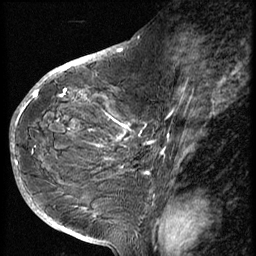
Breast MRI (dynamic contrast-enhanced), one sagittal slice; position 29 of 56 along the scan axis; 3 images stored at this slice position (order not interpretable as contrast timing); 1.5 T; TE 4.2 ms, TR 9 ms; 256 × 256 image matrix, field of view 180 × 180 mm. Patient: female, 49 years. Case-level facts recorded for this patient, not image findings: setting: breast cancer imaged before/during neoadjuvant chemotherapy; receptor status: HER2-positive.
Outlined on this slice (semi-automatically segmented with operator editing):
- analysis volume of interest (the breast-tissue region the enhancement analysis was run in; not a lesion): bounding box (x1, y1, x2, y2) in pixels: (37, 85, 132, 207)
- tumour enhancement mask (voxels above the 140 % enhancement threshold inside the analysis volume of interest): (37, 89, 131, 149)